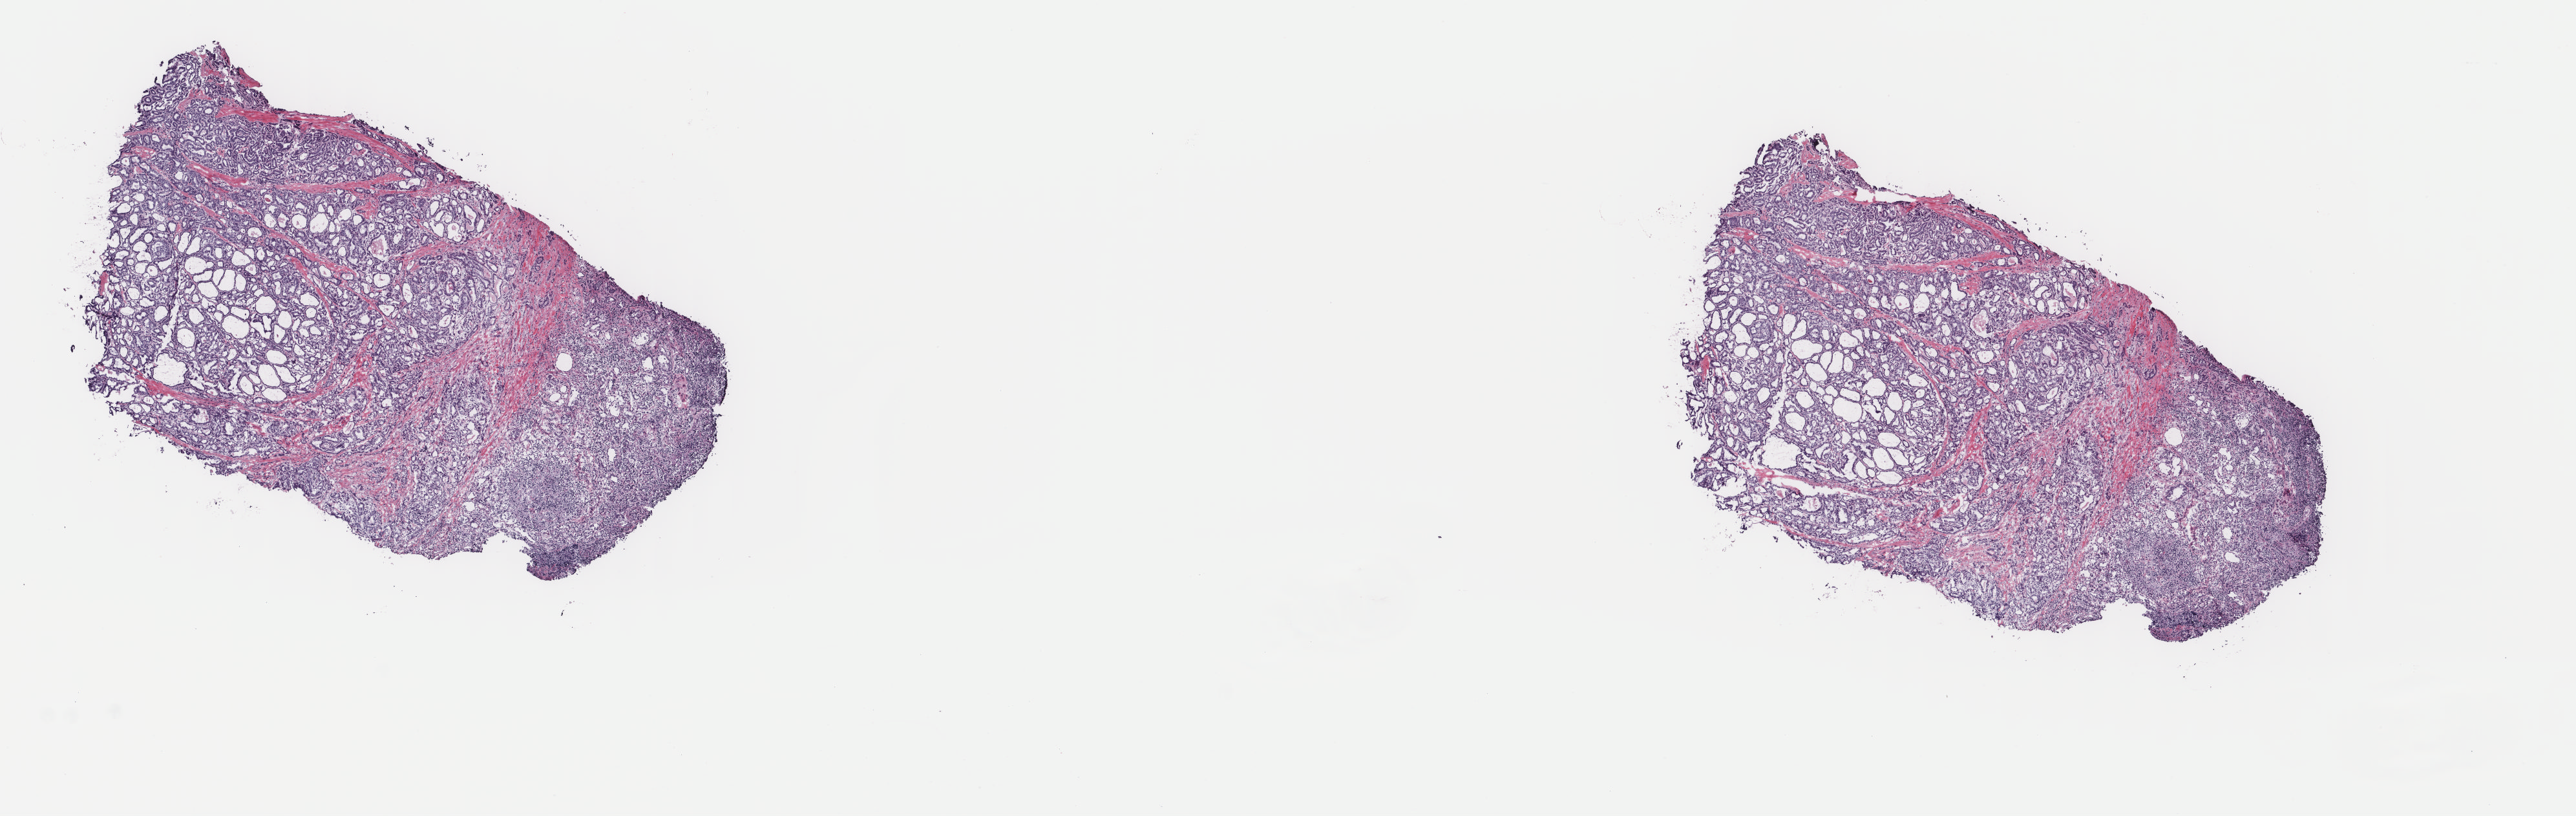
Digitized Hematoxylin and eosin (H&E) stained tissue section (whole slide), low-resolution overview of the scanned area, about 15.8 x 5.0 mm (slide scanned at 40x); frozen section from the top of the tissue portion; primary tumour sample from the thyroid. Patient: female, age at initial diagnosis 34 years. Composition of this section per pathologist review: tumour cells 70%, tumour nuclei 65%, normal cells 20%, stromal cells 10%, necrosis 0%. Infiltration values recorded for this section: lymphocyte infiltration 0%, monocyte infiltration 0%, neutrophil infiltration 0%.
- TNM: T1 N1a MX
- laterality: right
- AJCC pathologic stage: I (6th edition)
- lymph nodes positive (case pathology): 2 of 8 examined
- diagnosis: Papillary carcinoma, follicular variant (thyroid gland)